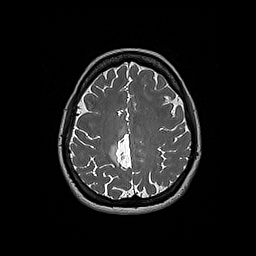
Brain MRI from a brain-tumour surgery series, one axial slice. Position 63 of 192 along the scan axis. 1 mm slice thickness. 256 × 256 image matrix. From the clinical record (not read from this slice): histopathology: Oligodendroglioma; WHO grade: 2; IDH mutation: yes; tumour location: Right Parietal.
Outlined on this slice (manually delineated by an expert):
- tumour: bounding box [x1, y1, x2, y2] px = [110, 143, 119, 166]